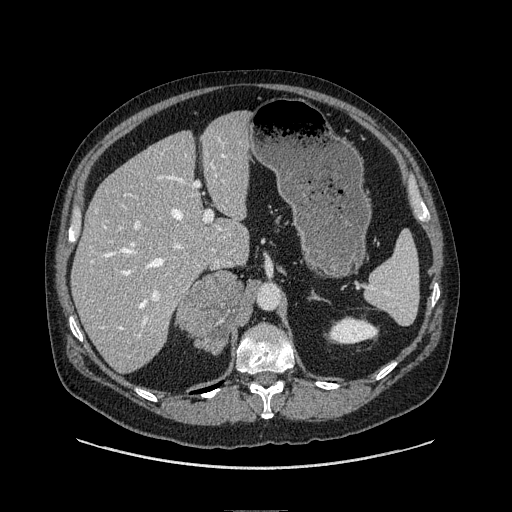
Contrast-enhanced abdominal CT, one axial slice; position 61 of 149 along the scan axis; soft-tissue window (W 400 / L 40 HU); 1.25 mm slice thickness; 512 × 512 image matrix. Male patient. Case-level facts recorded for this patient, not image findings: diagnosis: adrenocortical carcinoma; tumour side: right adrenal; tumour size at pathology: 7.5 cm; Ki-67 index: 15 %; stage (as recorded): 2.
Outlined on this slice (semi-automatically segmented with operator editing):
- mass: bounding box (x1, y1, x2, y2) in pixels: (177, 271, 244, 354)